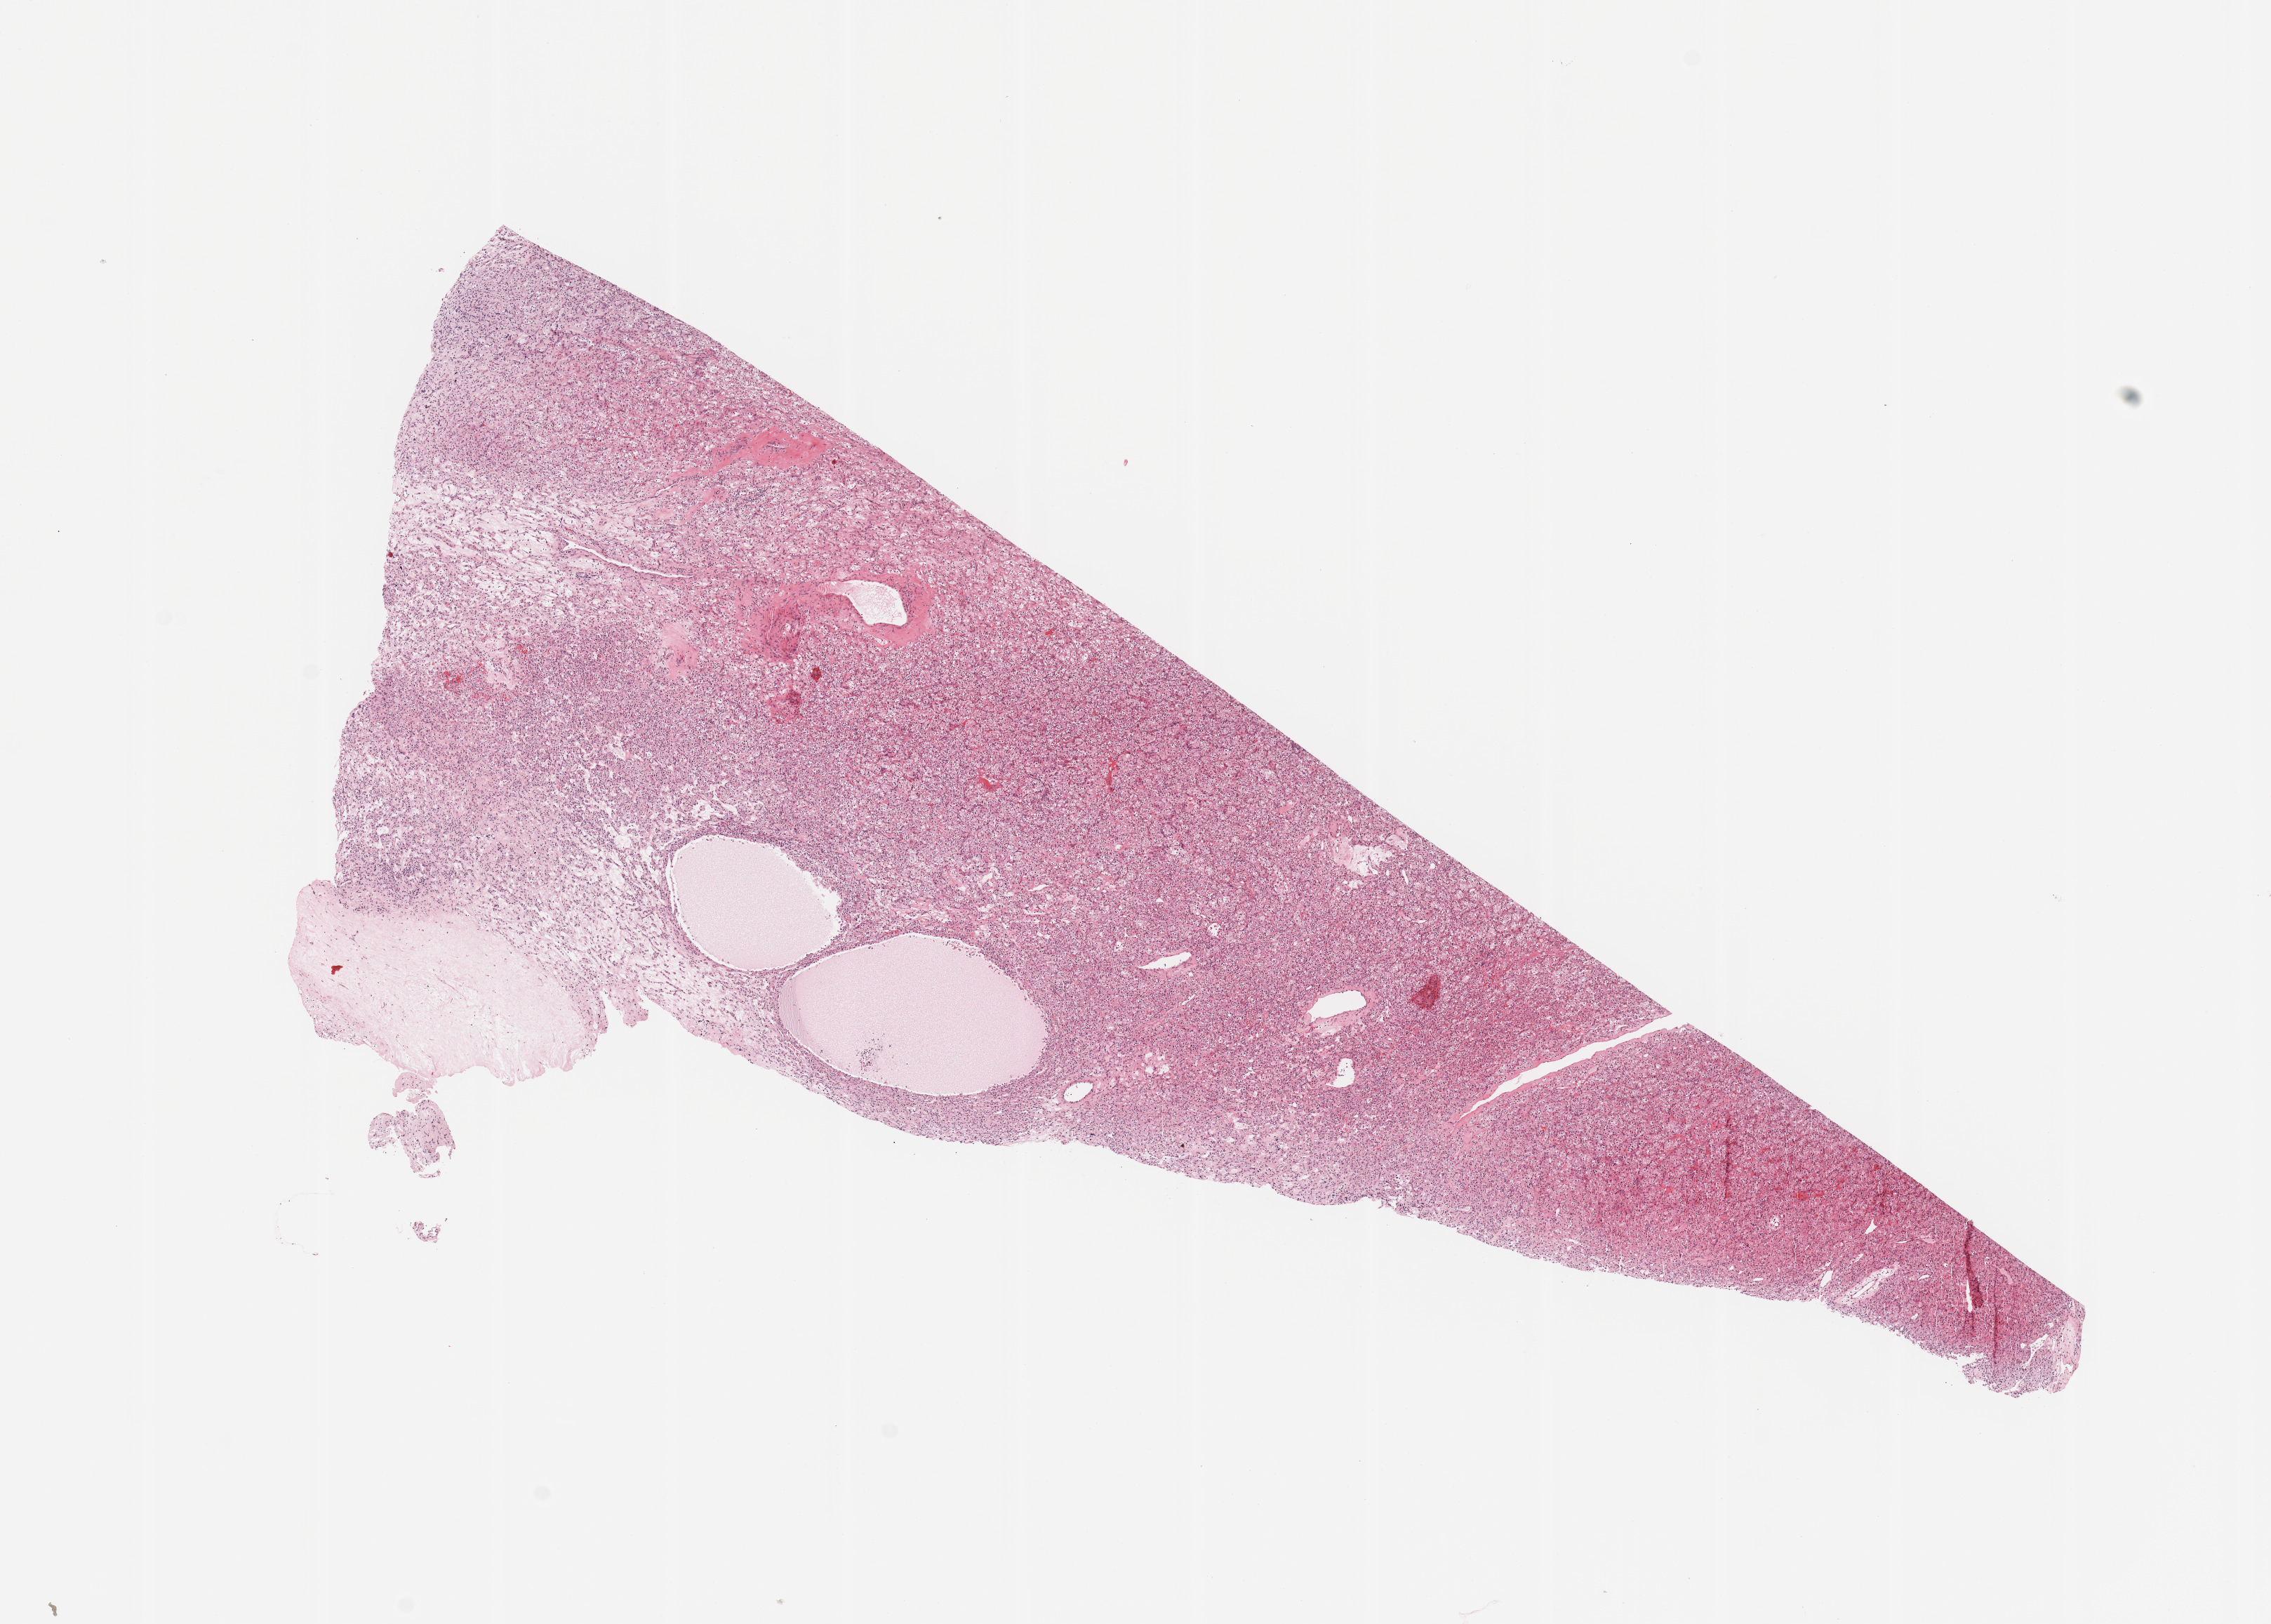
Whole-slide histology image, H&E-stained — shown as a low-resolution overview of the whole scanned area (about 12.8 x 9.2 mm, acquisition: 20x scan). Tumour tissue sample, sampled site: kidney. Patient: female, age 57 years. Histologic grade: G3 (poorly differentiated). Pathologist review of this section (percent, as recorded): tumour nuclei 90%, necrosis 5%.
AJCC pathologic stage: I. Diagnosis: Renal cell carcinoma, NOS.